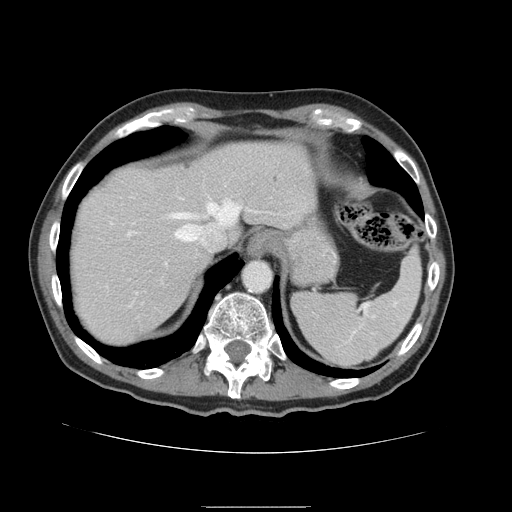
Contrast-enhanced abdominal CT, one axial slice. Slice 124 of 168 in the series (ordered by position). 120 kVp. Intravenous contrast given. Soft-tissue window (W 400 / L 40 HU). 512 × 512 image matrix, field of view 386 × 386 mm. Male patient, age 74 years. Case-level facts recorded for this patient, not image findings: diagnosis: colorectal cancer liver metastases, imaged before liver resection; multiple liver metastases: no.
Annotated regions visible in this slice (outlined manually by an expert reader):
- hepatic veins: bounding box (x1, y1, x2, y2) in pixels: (173, 202, 239, 245)
- liver: (70, 142, 315, 347)
- planned liver remnant (the part of the liver to remain after resection): (69, 142, 316, 346)